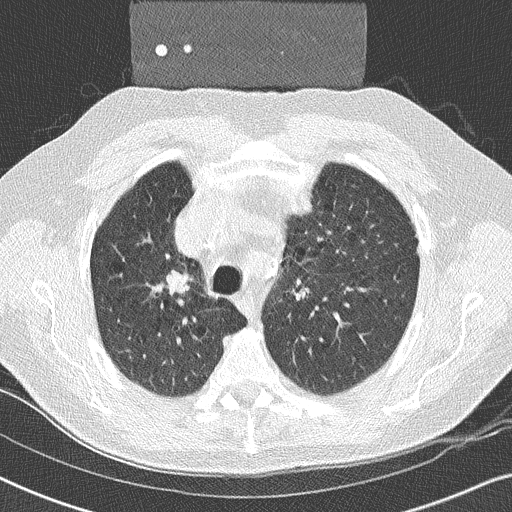
Chest CT (low-dose screening protocol), one axial image; second annual screen; lung window (W 1500 / L -600 HU); 2 mm slice thickness; lung (sharp) reconstruction kernel (B50f); 120 kVp. Male, age 59 years at enrolment. Former smoker at enrolment.
Expert-annotated lung lesion, bounding box [x1, y1, x2, y2] px = [150, 259, 207, 308]. The exam's reader record, not a measurement of the box and not confirmed to be the same lesion: non-calcified nodule or mass ≥4 mm, right upper lobe, 17 × 16 mm, smooth margins, soft tissue attenuation, pre-existing on the prior screen: yes. Official screen result: positive, other.